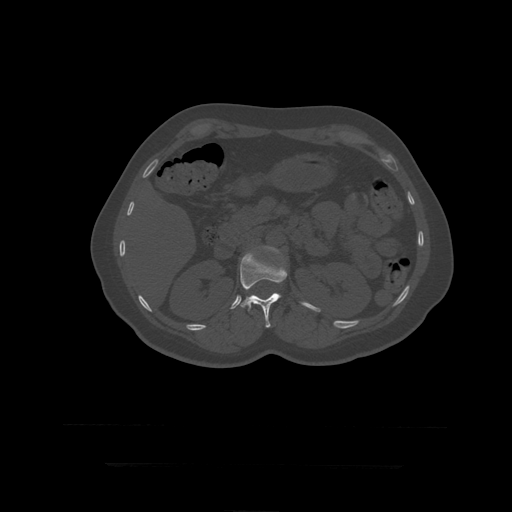
CT including the spine, one axial slice. Bone window (W 1800 / L 400 HU). 512 × 512 image matrix, field of view 450 × 450 mm. Patient age 41 years. From the clinical record (not read from this slice): primary cancer: breast.
Structures marked on this image (semi-automatic segmentation, software-assisted and operator-edited):
- L1 vertebra: bounding box [x1, y1, x2, y2] px = [240, 252, 288, 328]
- L2 vertebra: [264, 246, 279, 253]